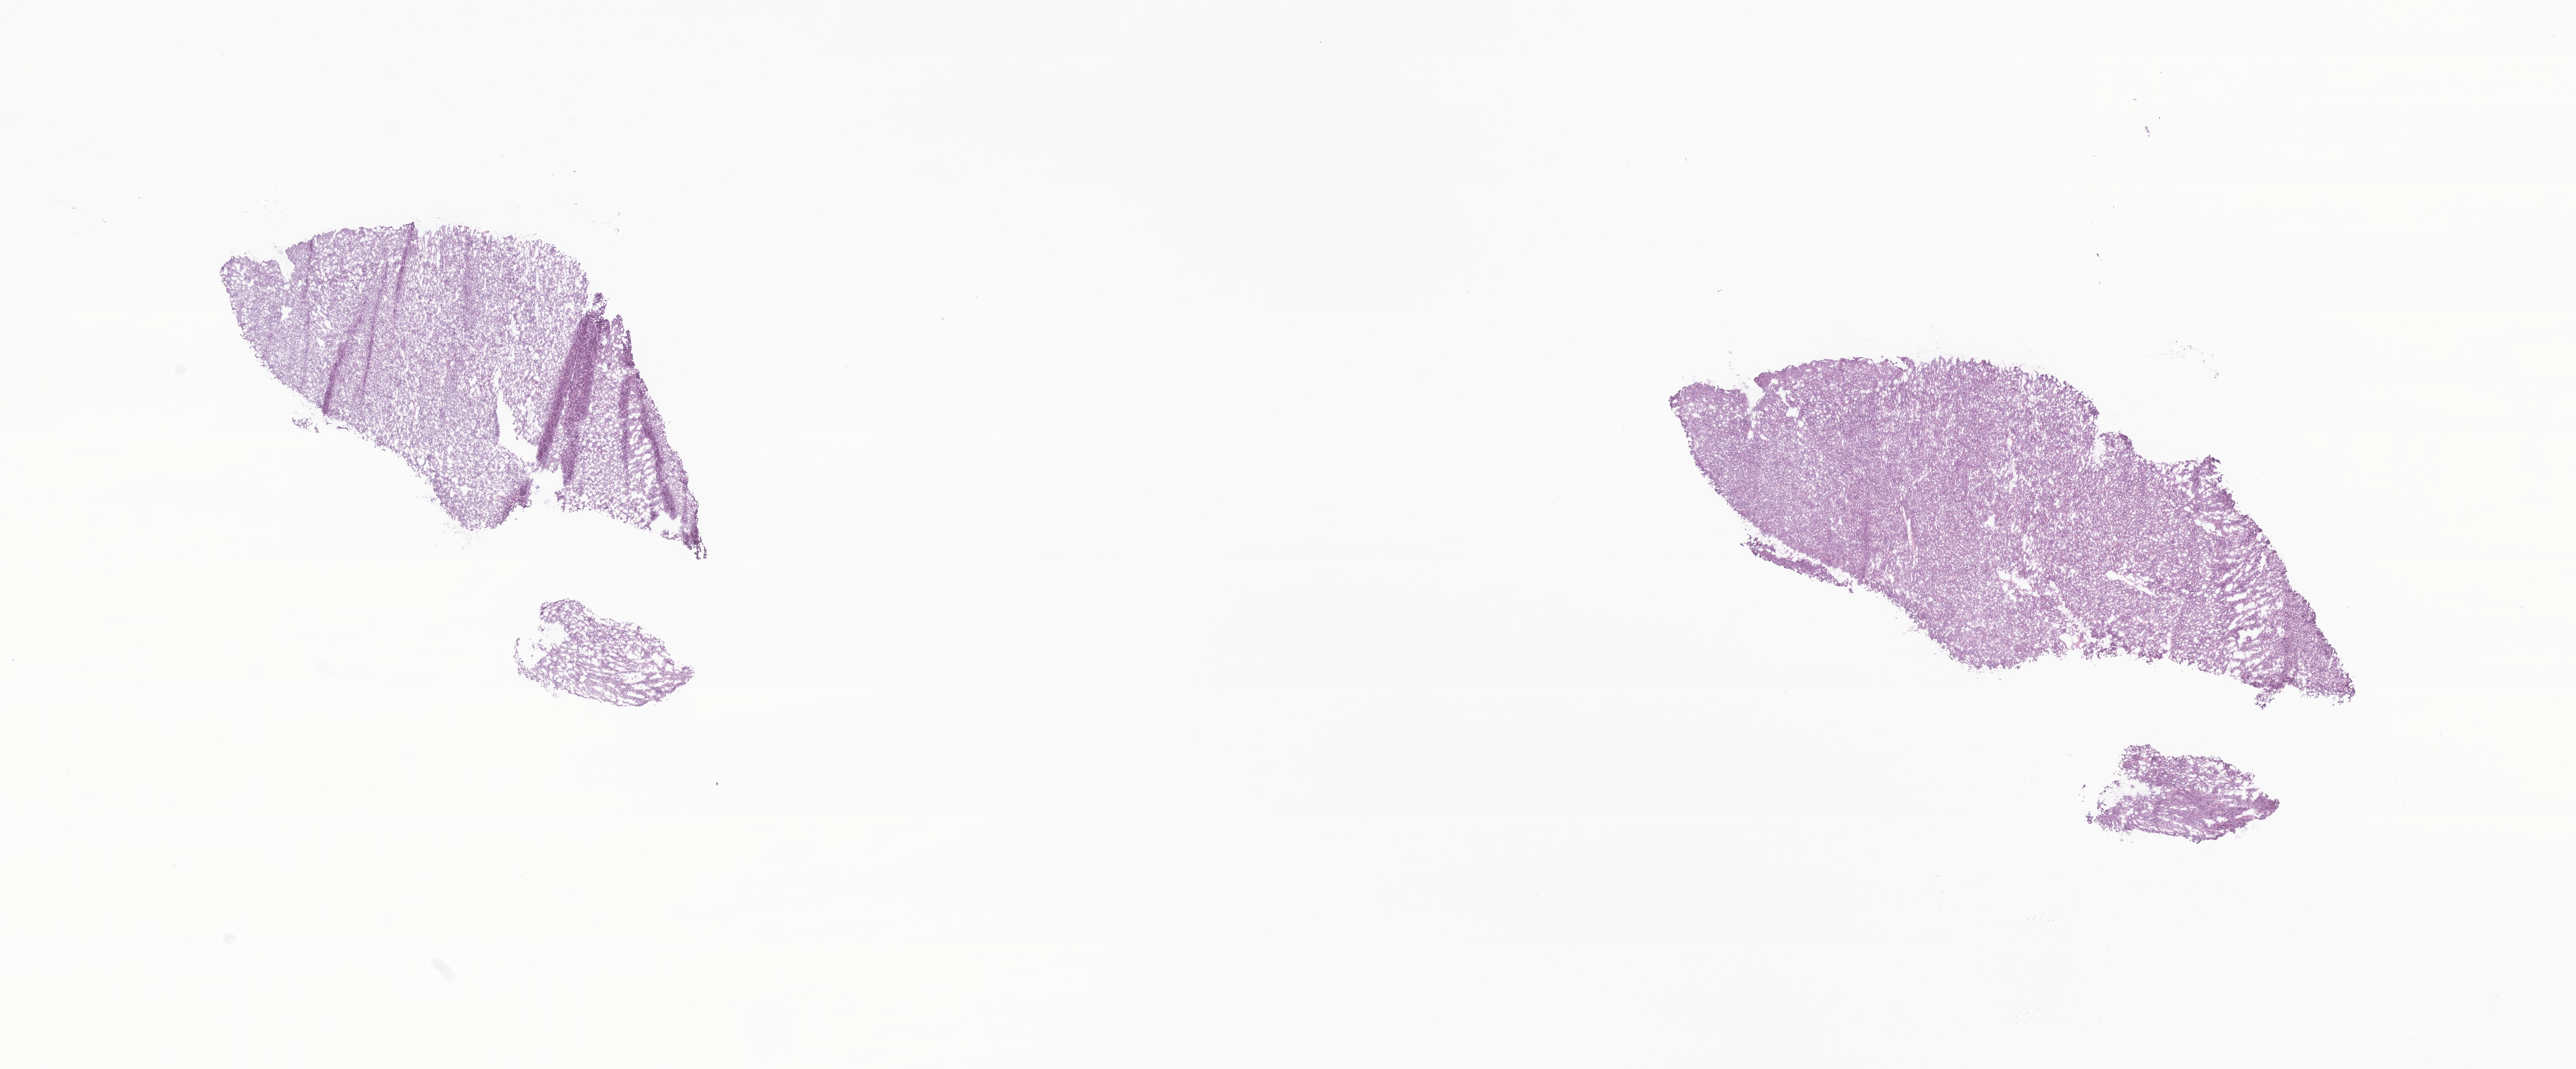
Digitized hematoxylin and eosin (H&E)-stained section of tumor tissue from the greater curvature of stomach, shown as a low-resolution overview of the whole scanned area (about 21.6 x 9.0 mm). Patient: female, age 236 months (19 years 8 months).
• specimen: frozen section (OCT-embedded)